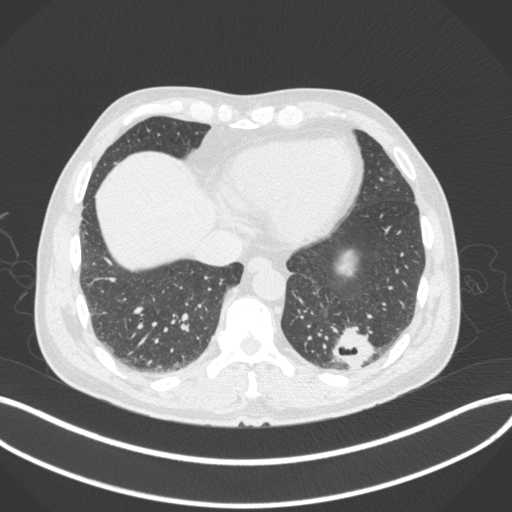
Chest CT, one axial slice. Position 71 of 313 along the scan axis. Reconstruction kernel B31f. Lung window (W 1500 / L -600 HU). 512 × 512 image matrix, field of view 400 × 400 mm. Patient: male, 54 years. From the clinical record (not read from this slice): clinical TNM (as recorded): T1c N0 M1; histopathological grade: G3.
Structures marked on this image (bounding box drawn by a radiologist):
- lung tumour (recorded histology: adenocarcinoma): bounding box (x1, y1, x2, y2) in pixels: (326, 326, 379, 371)